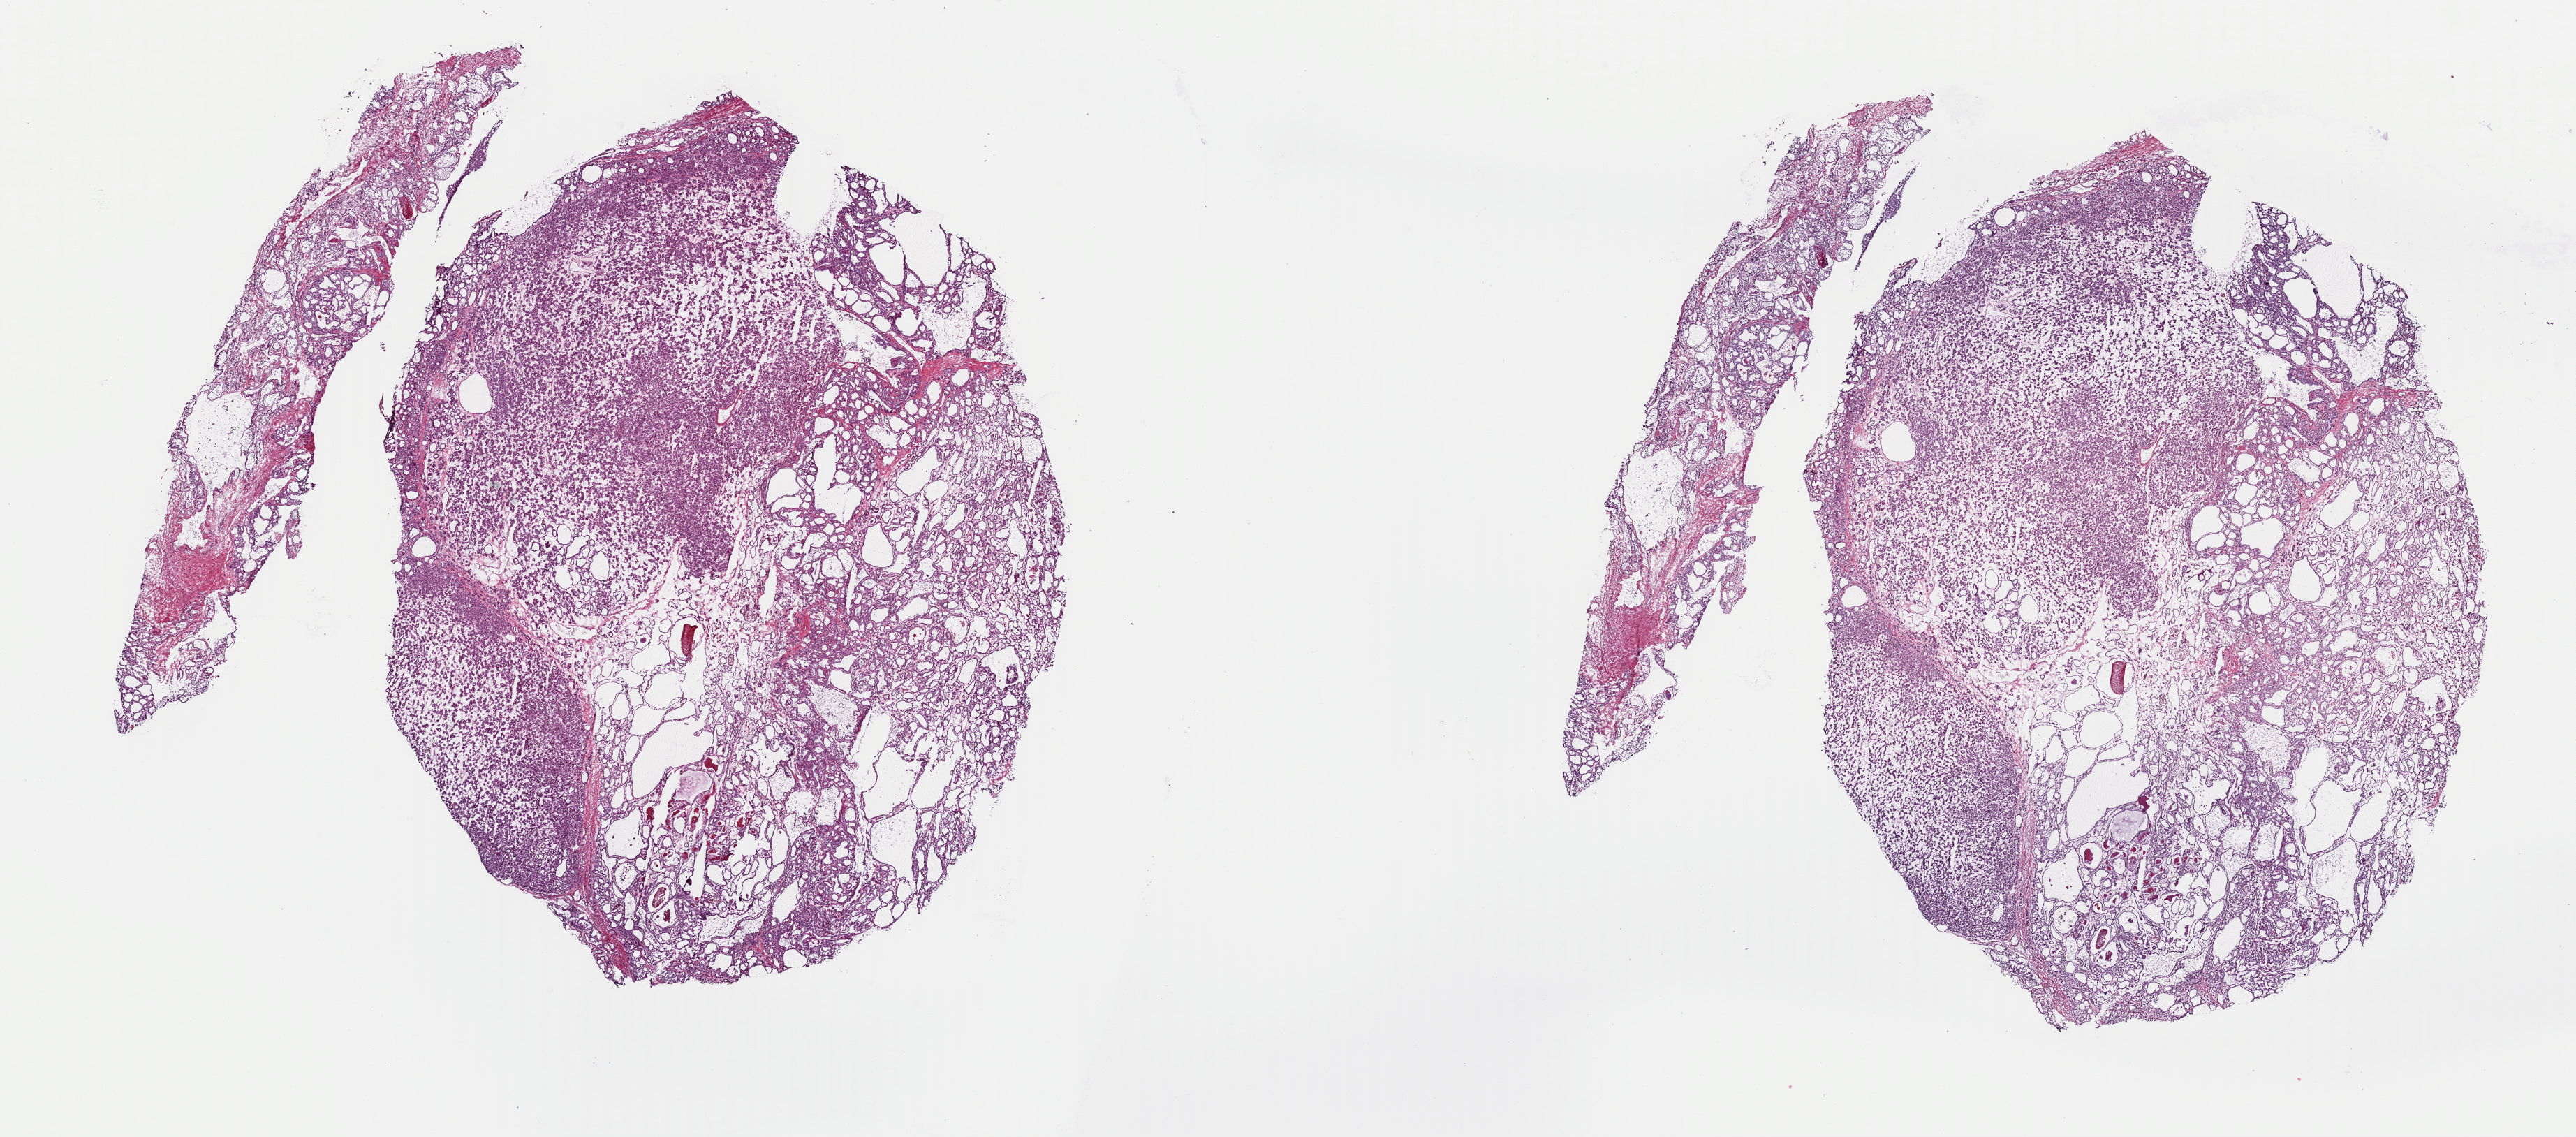
H&E whole-slide image, shown as a low-resolution overview of the whole scanned area (about 29.1 x 12.9 mm), frozen section from the top of the tissue portion, thyroid, primary tumour sample. Female, age 43 years at initial diagnosis. Composition of this section per pathologist review: tumour cells 90%, tumour nuclei 90%, normal cells 10%, stromal cells 0%, necrosis 0%. Inflammatory infiltration, as recorded: lymphocyte infiltration 0%, monocyte infiltration 0%, neutrophil infiltration 0%.
AJCC pathologic stage: I. Histologic diagnosis: Papillary carcinoma, follicular variant (thyroid gland).